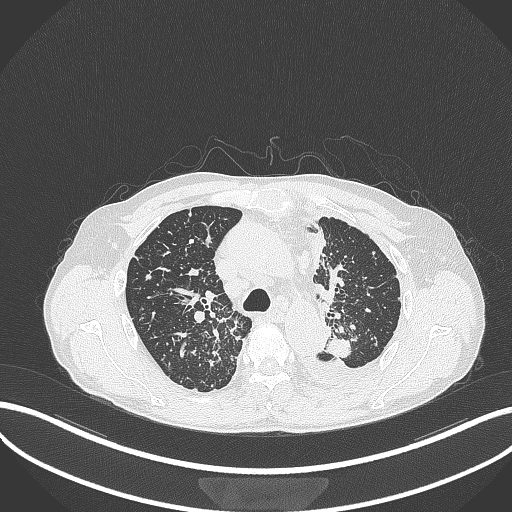
Chest CT, one axial slice; position 253 of 325 along the scan axis; reconstruction kernel B70f; 120 kVp; lung window (W 1500 / L -600 HU); 512 × 512 image matrix. Patient: male, 58 years. From the clinical record (not read from this slice): clinical TNM (as recorded): T1c N3 M1.
Outlined on this slice (bounding box drawn by a radiologist):
- lung tumour (recorded histology: adenocarcinoma): bounding box [x1, y1, x2, y2] px = [322, 335, 353, 357]